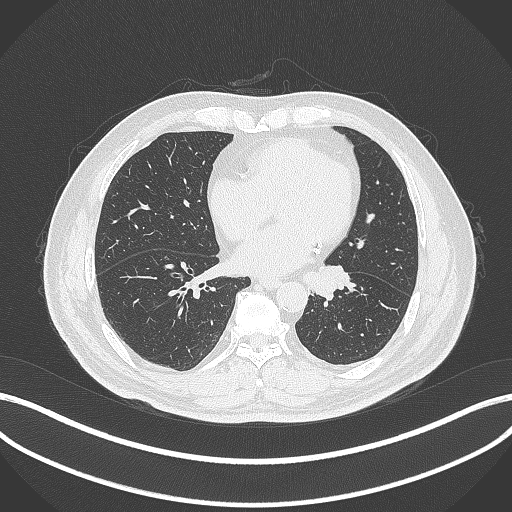
Chest CT, one axial slice; slice 108 of 312 in the series (ordered by position); lung window (W 1500 / L -600 HU); 1 mm slice thickness; 512 × 512 image matrix. Patient: male, 71 years. From the clinical record (not read from this slice): clinical TNM (as recorded): T1b N0 M0.
Annotated regions visible in this slice (rectangle marked by the reading radiologist):
- lung tumour (recorded histology: squamous cell carcinoma): bounding box [x1, y1, x2, y2] px = [303, 266, 351, 301]